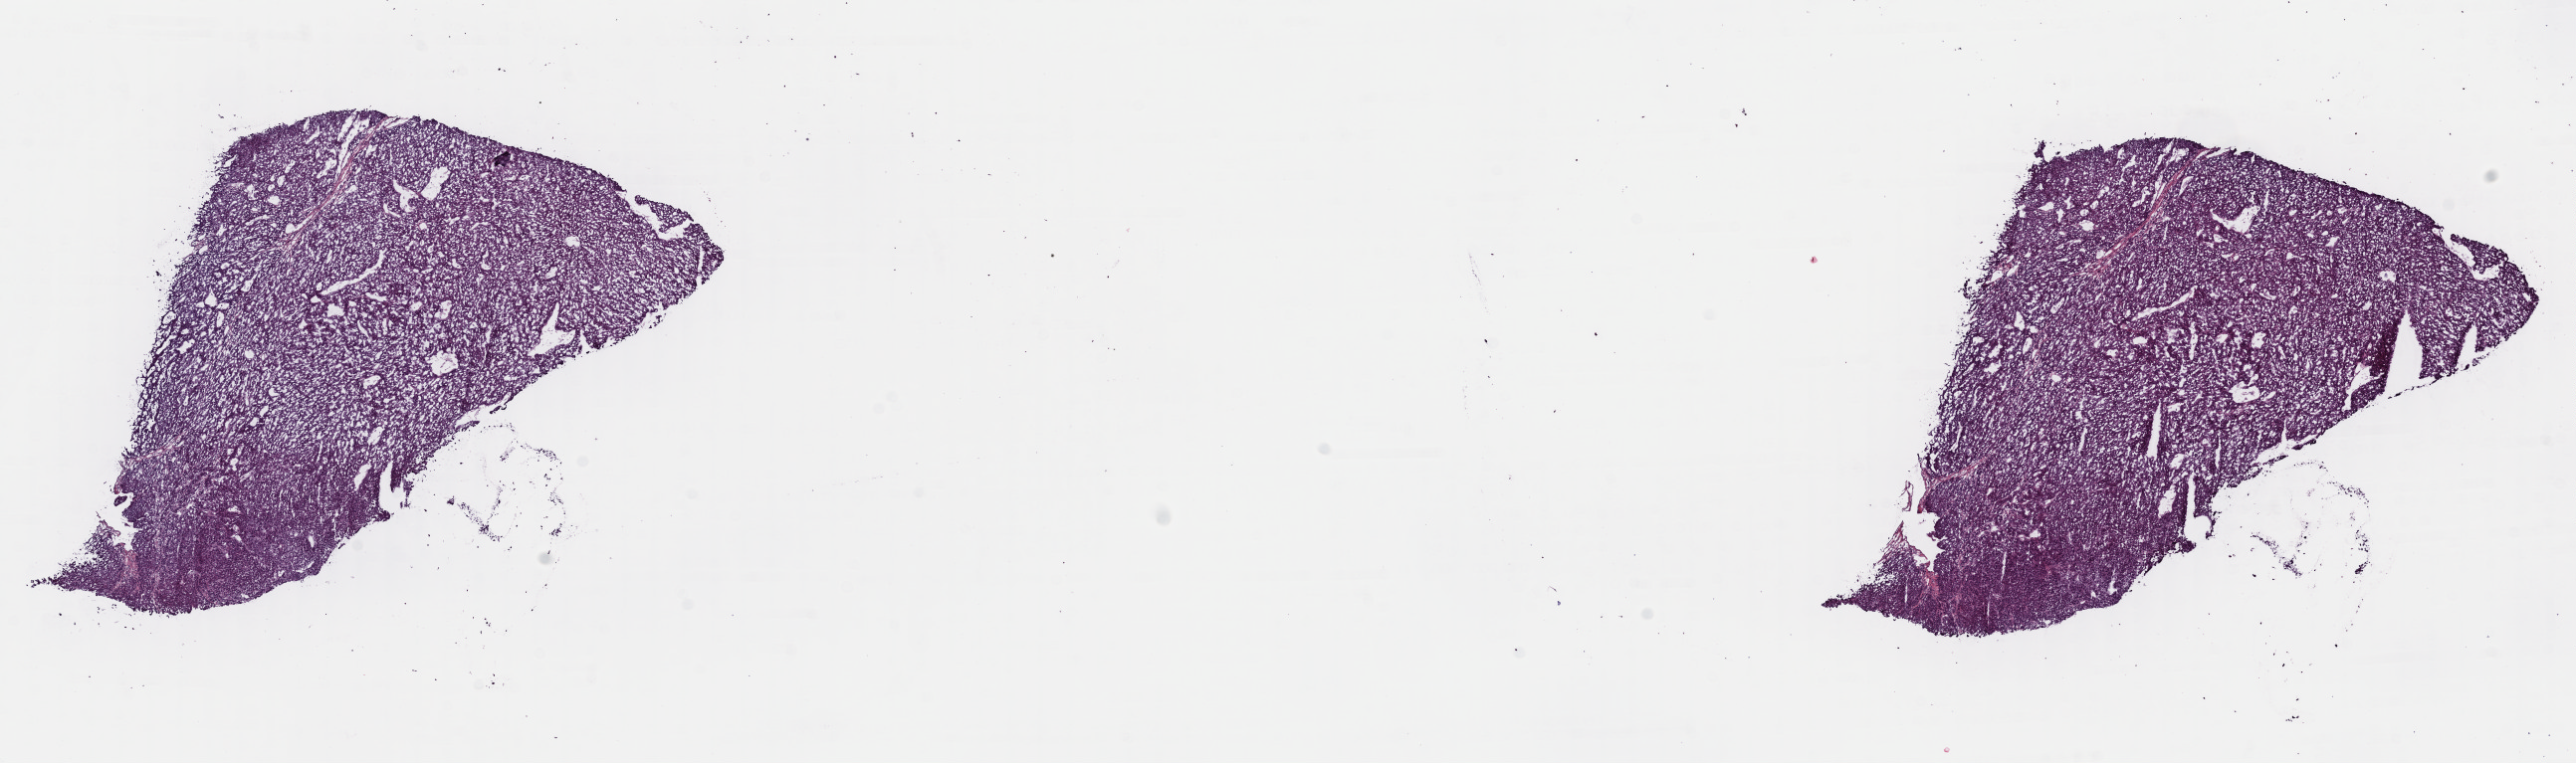
H&E whole-slide image, a low-resolution overview of the entire scanned area, about 20.4 x 6.1 mm. Frozen section from the top of the tissue portion. Adrenal cortex, primary tumour sample. Patient: female, age at initial diagnosis 48 years. Slide review estimates, as recorded: tumour cells 90%, tumour nuclei 95%.
Histologic diagnosis: Adrenal cortical carcinoma (cortex of adrenal gland).